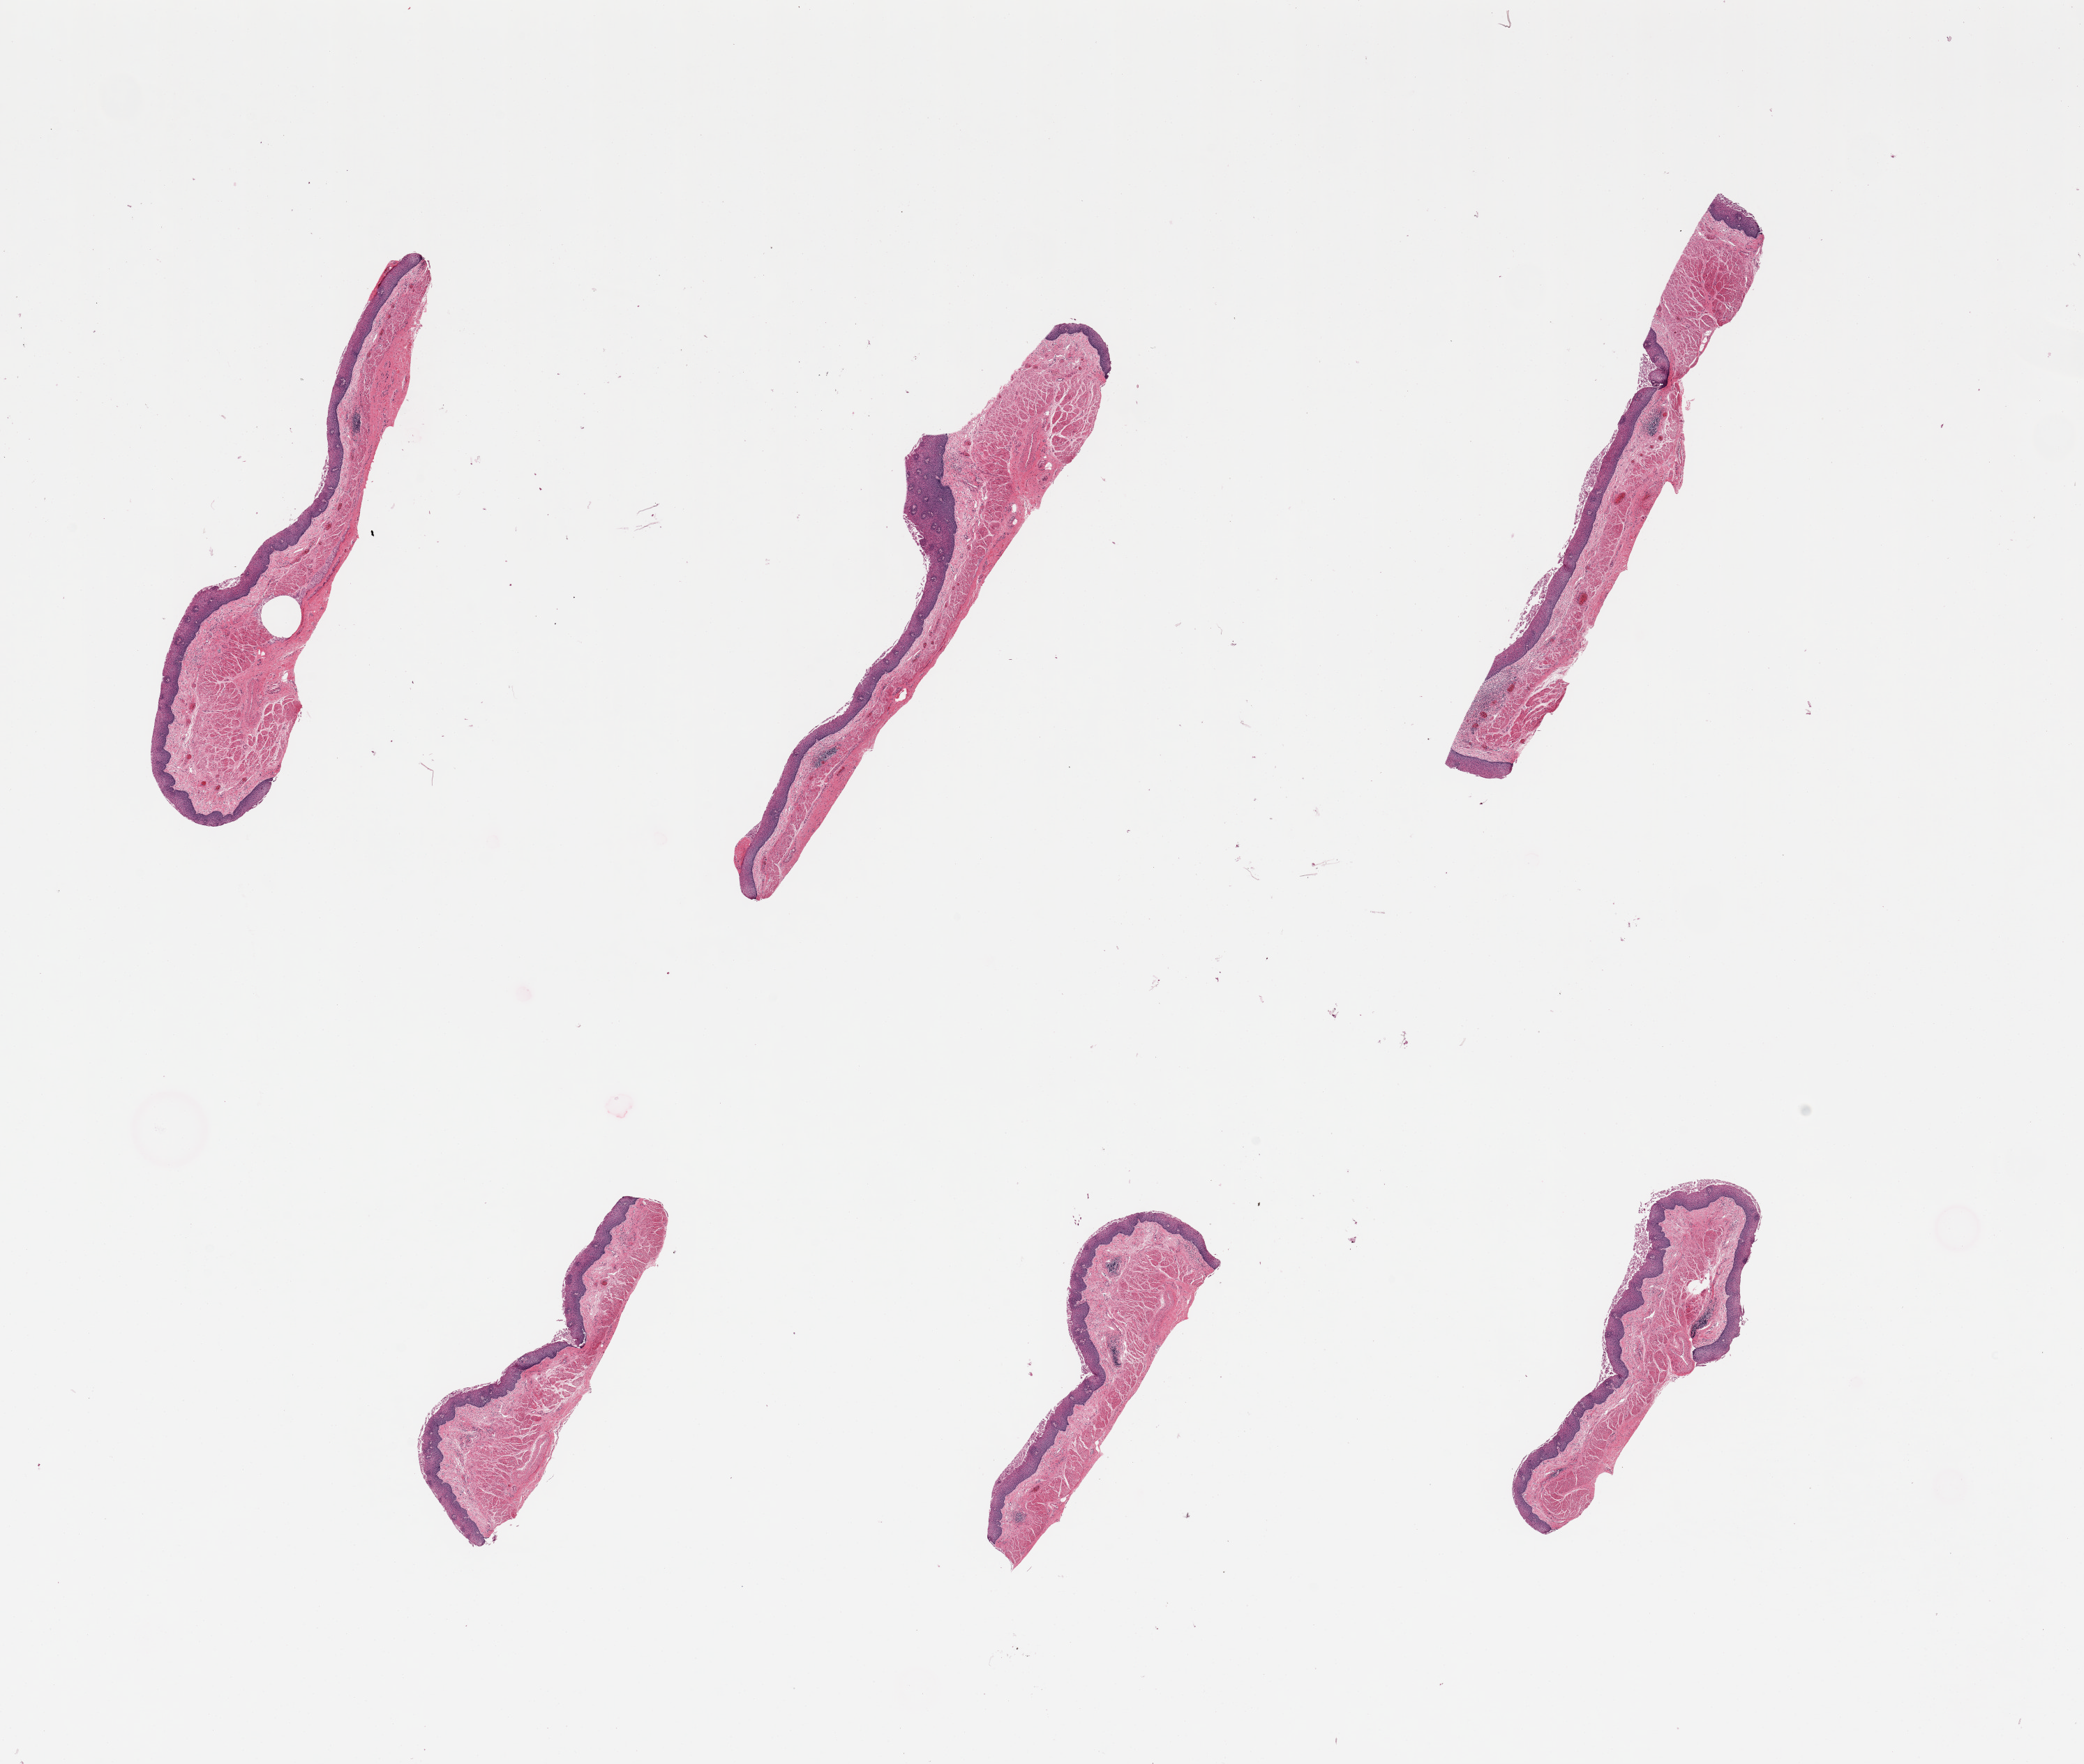
Whole-slide image, H&E stain — shown as a low-resolution overview of the whole scanned area (about 23.6 x 20.0 mm), PAXgene-fixed, paraffin-embedded tissue, target tissue: esophageal mucous membrane, donor tissue sample.
Reviewer comment on this tissue sample: 6 pieces, well trimmed.